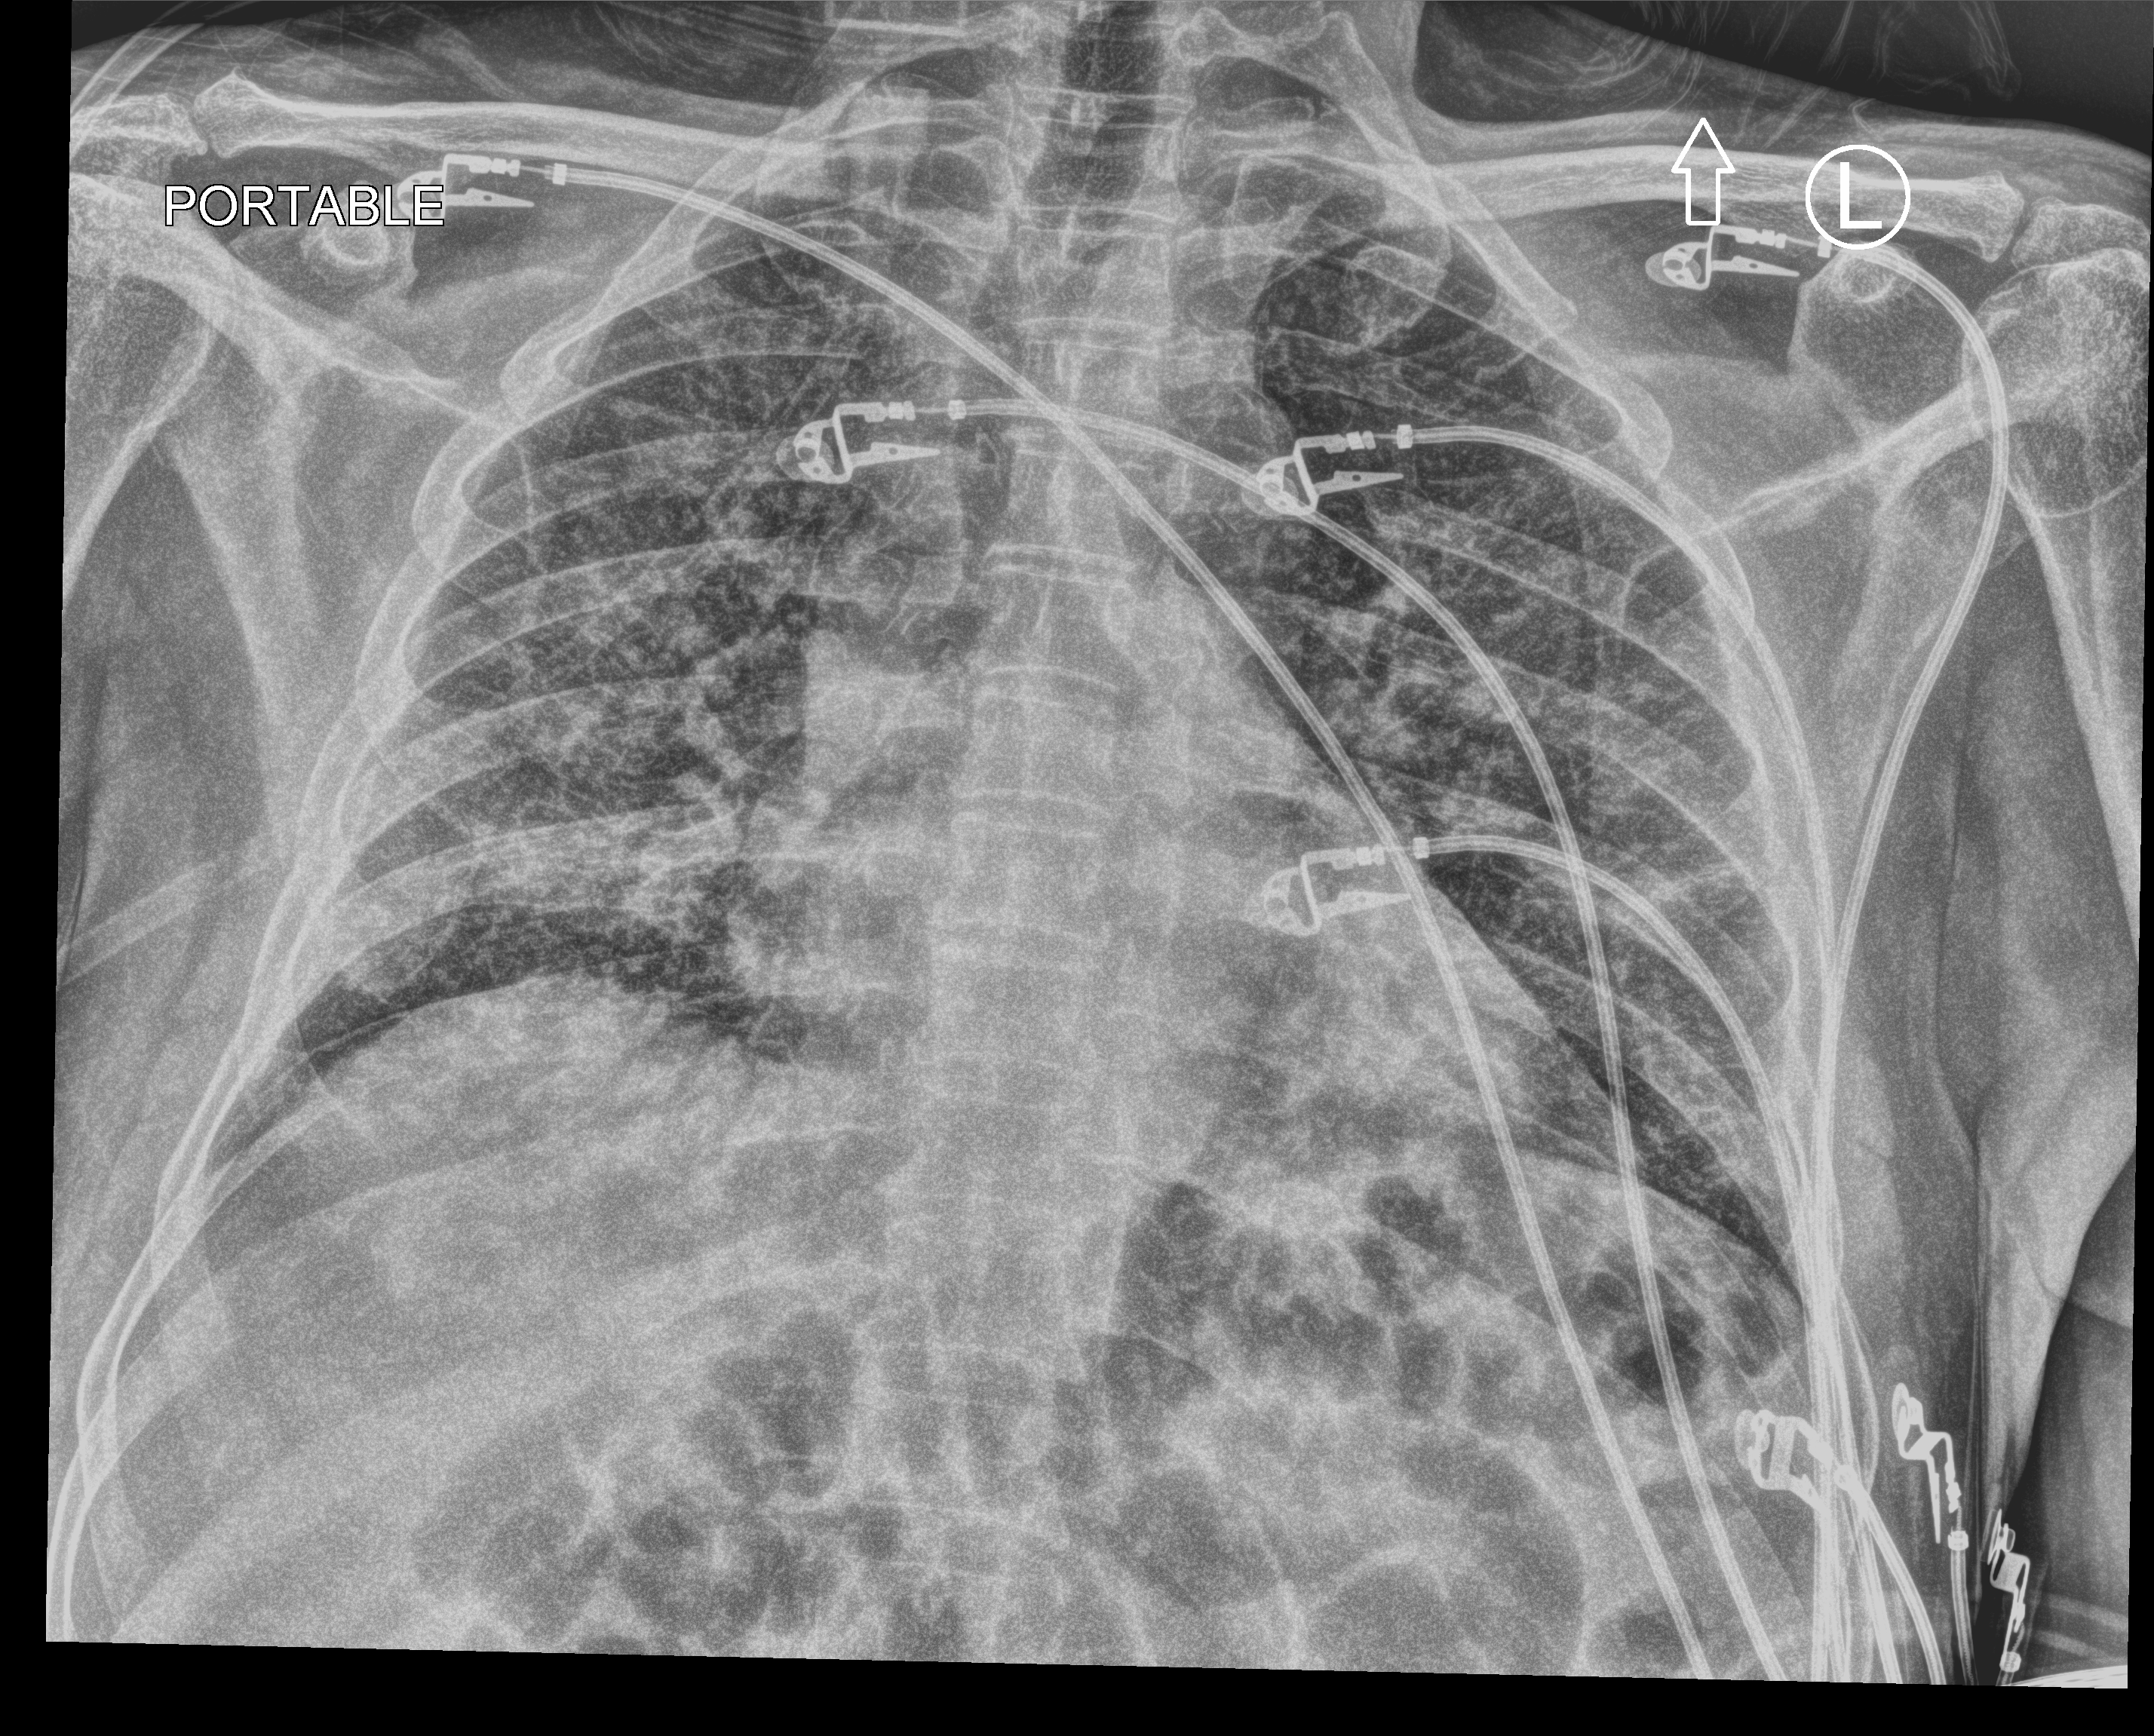
Bedside chest radiograph (computed radiography), anteroposterior (AP) projection. Male patient hospitalised with COVID-19, age 60–74 years.
Hospital-stay facts (about this admission, not read from this image; timing relative to this image not recorded): smoking status (admission record): never; COPD (admission record): no.